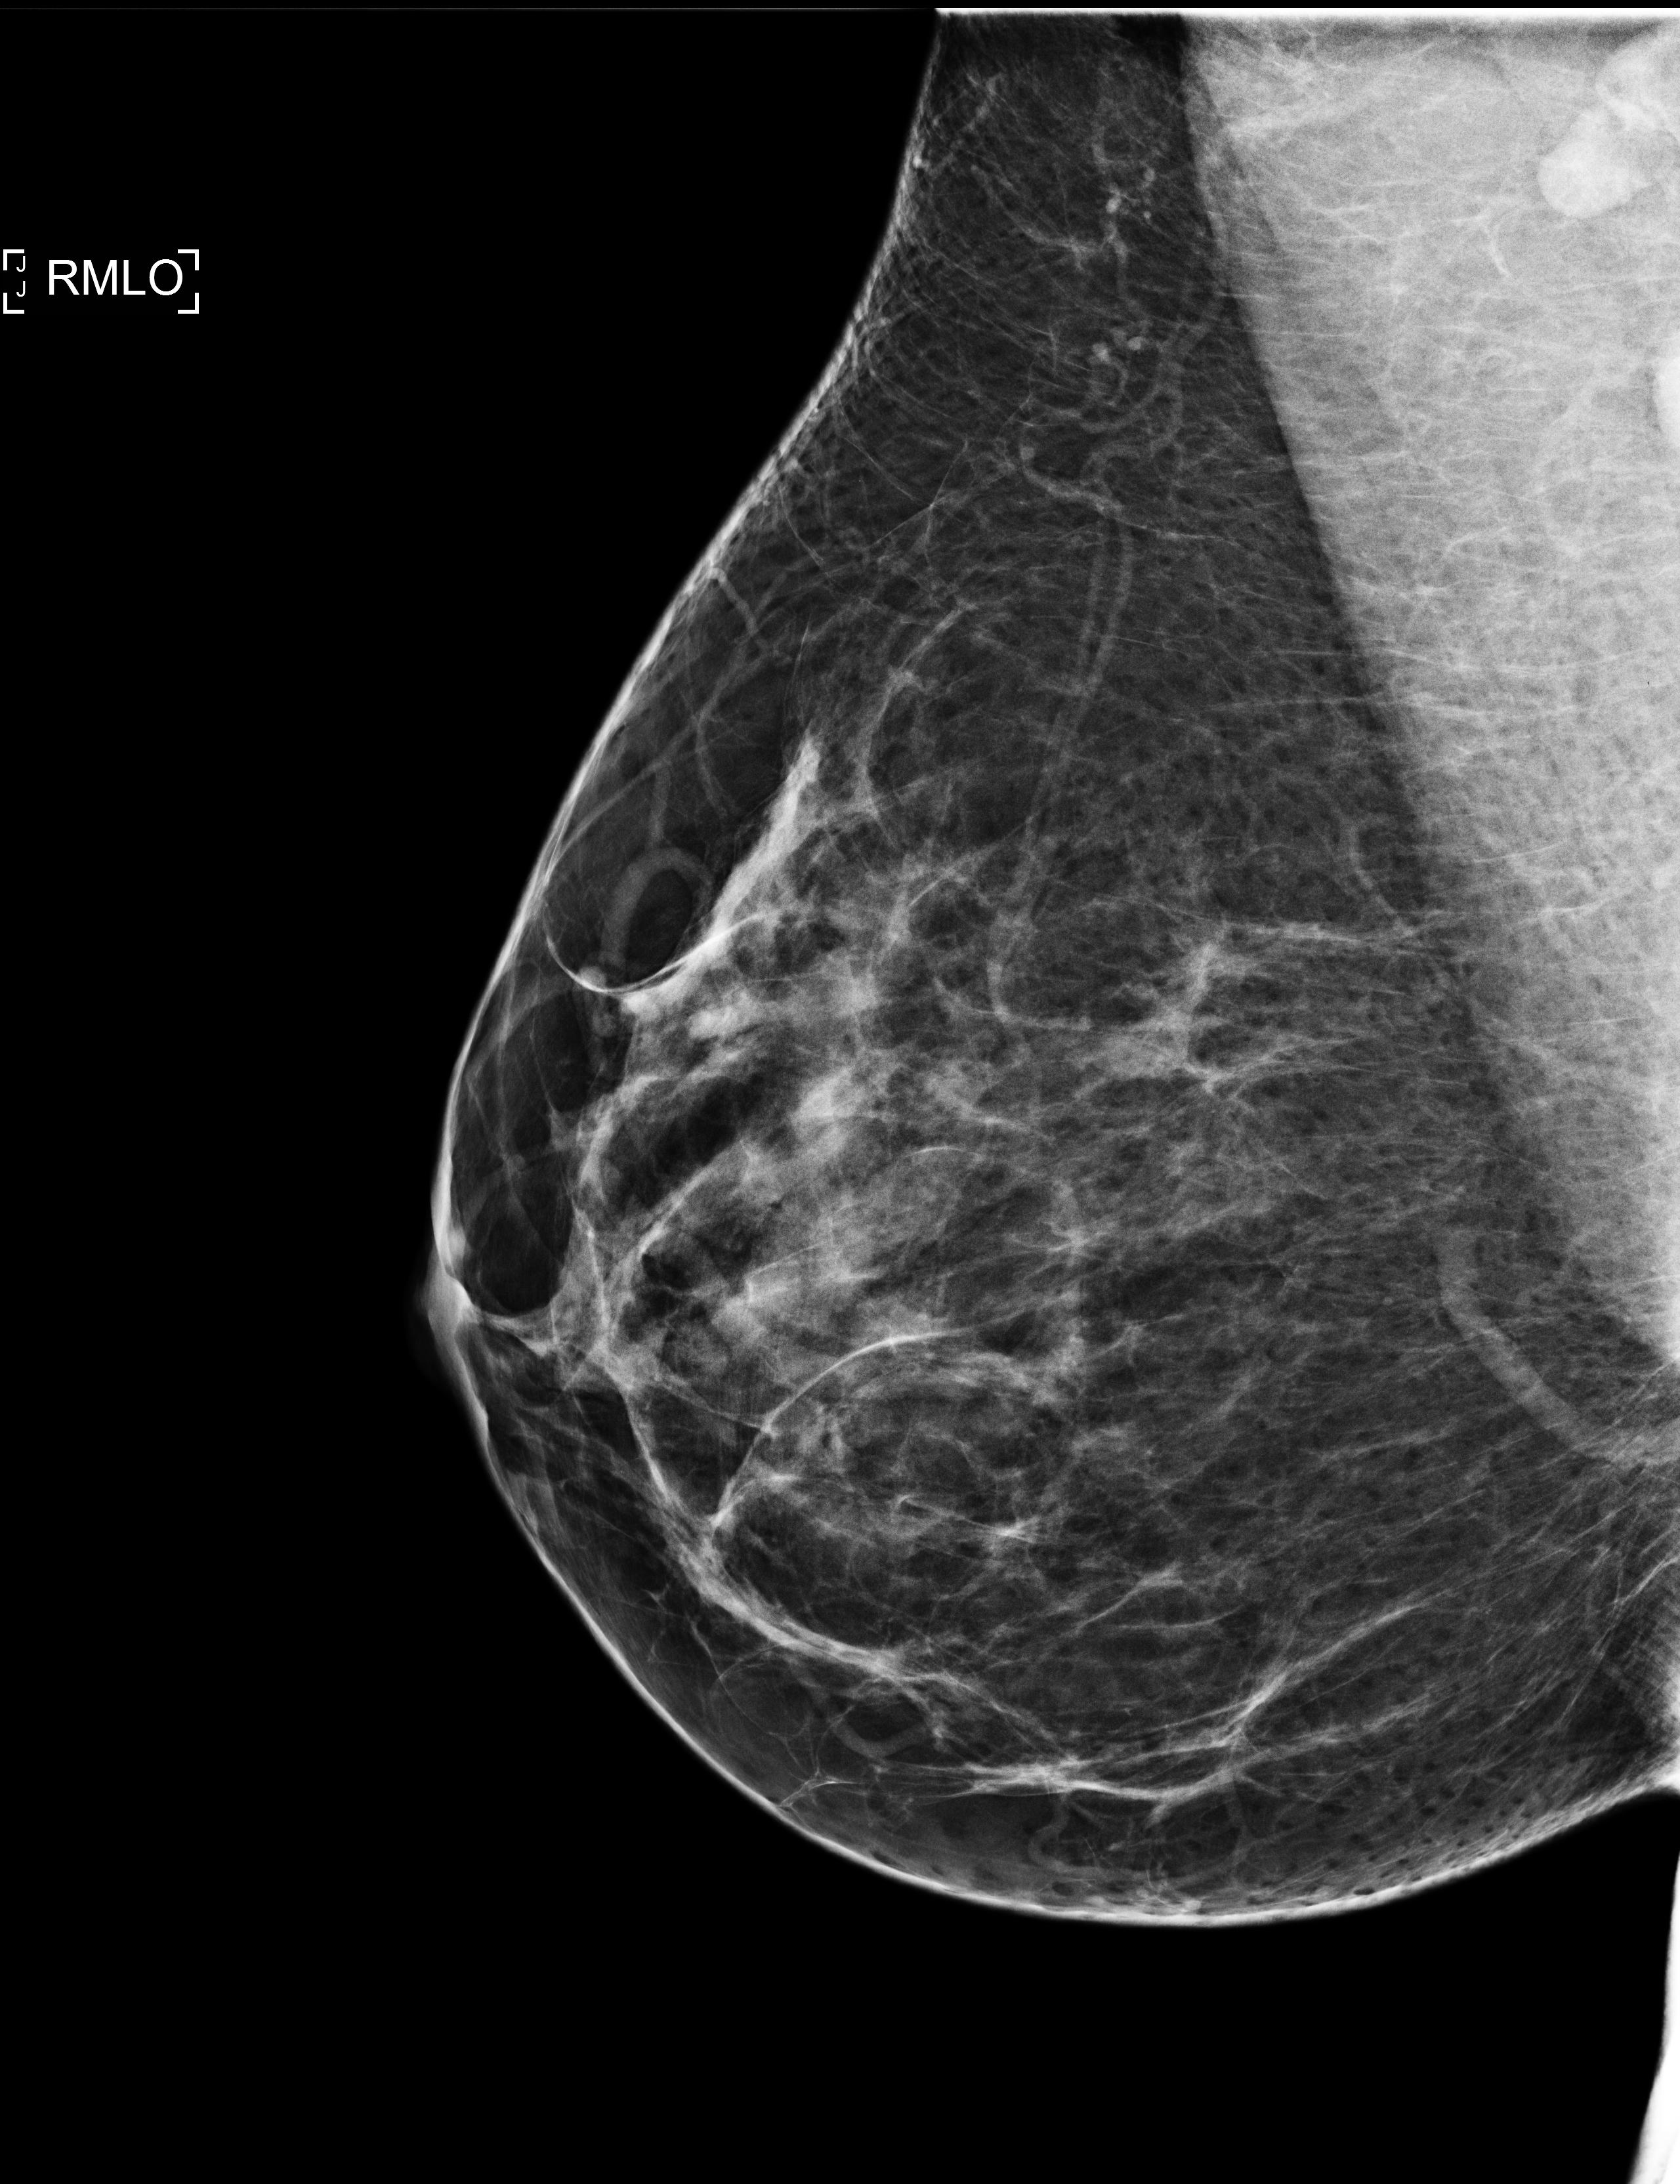
Digital mammogram (FFDM); right breast; mediolateral oblique (MLO) view; screening examination. Female patient, age 41 years.
- BI-RADS breast density category at the screening exam (both breasts, scale 1–4): 2
- final BI-RADS assessment for this screening round (tomosynthesis exam, both breasts): category 1
- recall: no recall after this screen